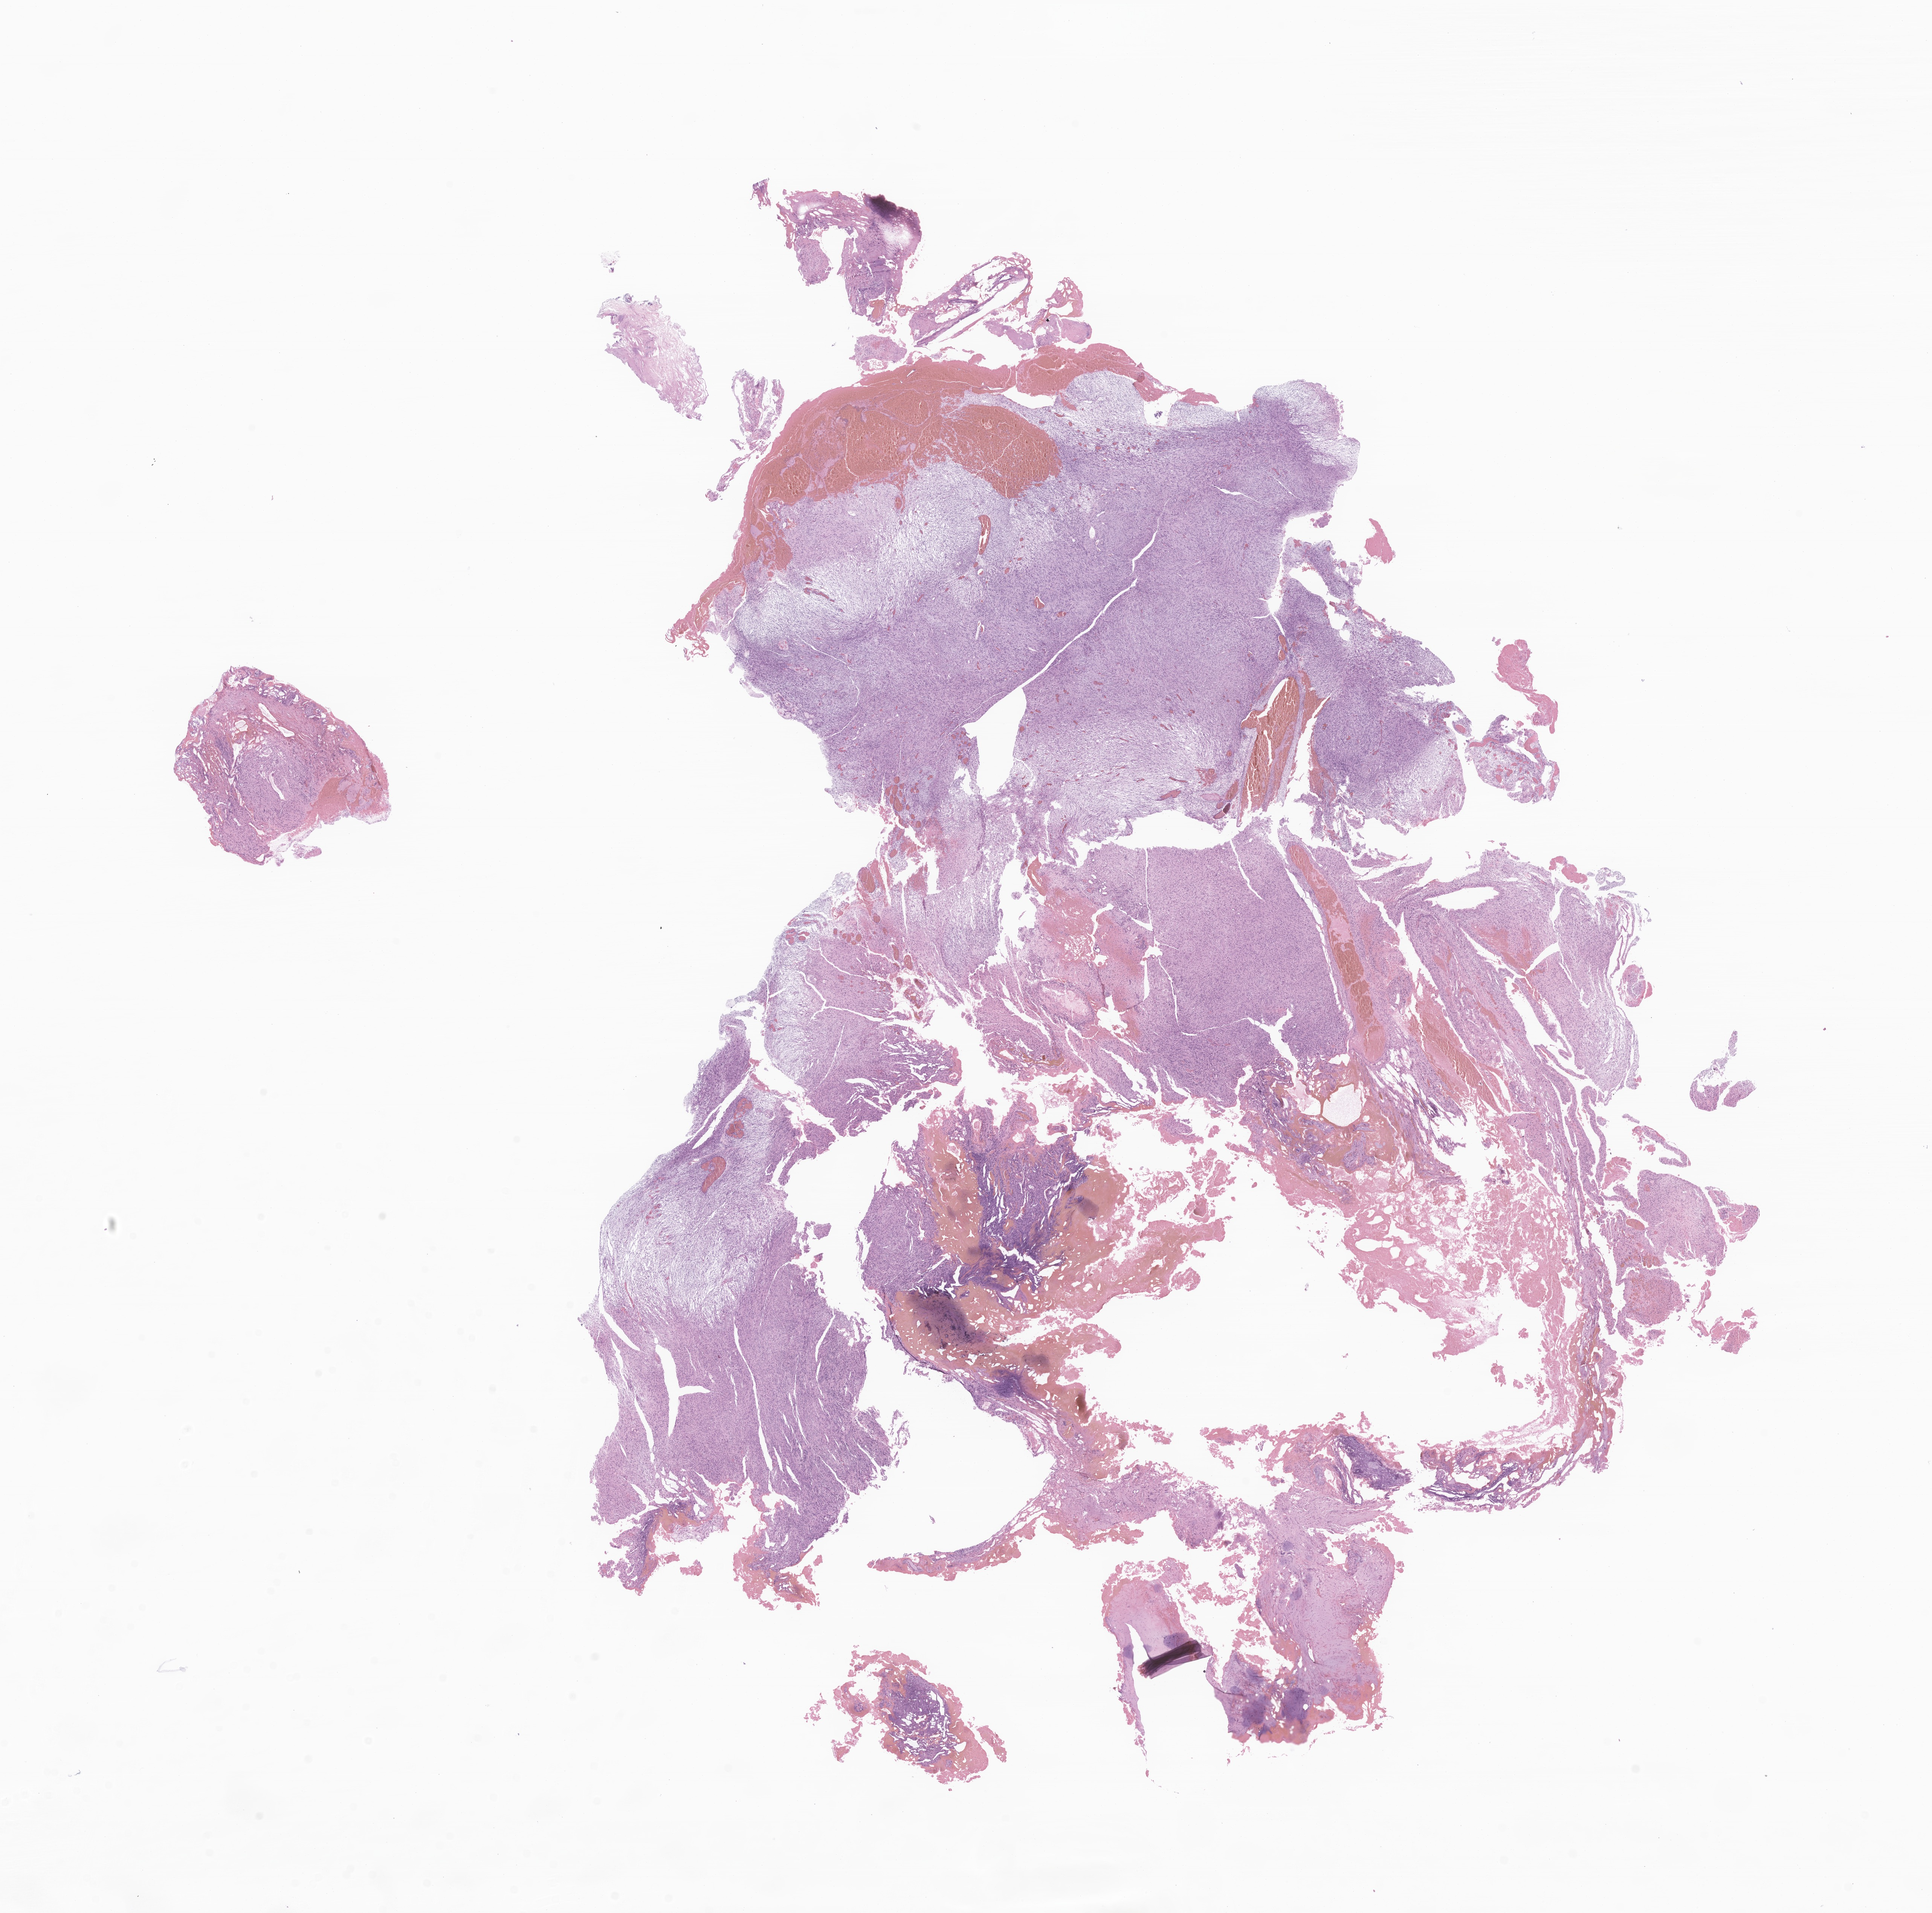
H&E whole-slide image of tumor tissue from the brain — a low-resolution overview of the entire scanned area, about 21.6 x 21.4 mm; FFPE section. Patient: male, age 119 months (9 years 11 months).
• diagnosis: Neuroma, NOS